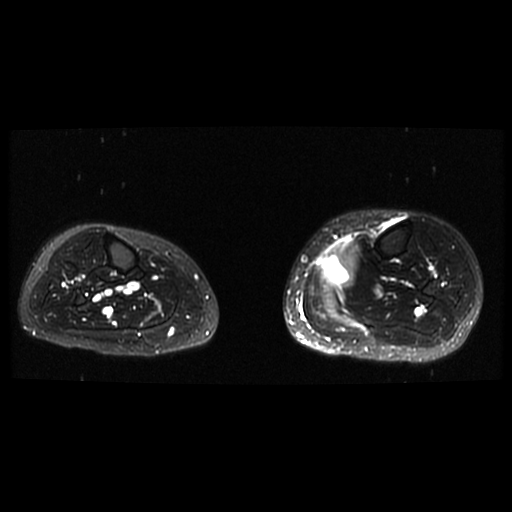
MRI of an extremity soft-tissue mass, one axial slice. Slice 10 of 38 in the series (ordered by position). T2-weighted fat-saturated. 6 mm slice thickness. 512 × 512 image matrix, field of view 330 × 330 mm. Female patient. From the clinical record (not read from this slice): histological type: extraskeletal high grade osteogenic sarcoma; grade: high; site of the primary tumour: left calf.
Outlined on this slice (outlined manually by an expert reader):
- gross tumour volume (mass): box from (x=320, y=242) to (x=361, y=289) px